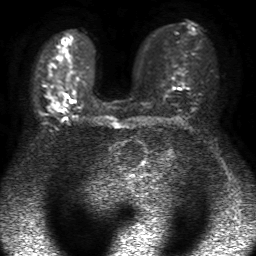
Breast MRI, one axial slice. Slice 29 of 50 in the series (ordered by position). Diffusion-weighted series; image 2 of 4 stored at this slice position (different b-values; order by instance number). 1.5 T. 256 × 256 image matrix, field of view 320 × 320 mm. Female patient.
Annotated regions visible in this slice (manually delineated by an expert):
- tumour on diffusion-weighted imaging: bounding box (x1, y1, x2, y2) in pixels: (52, 99, 62, 110)